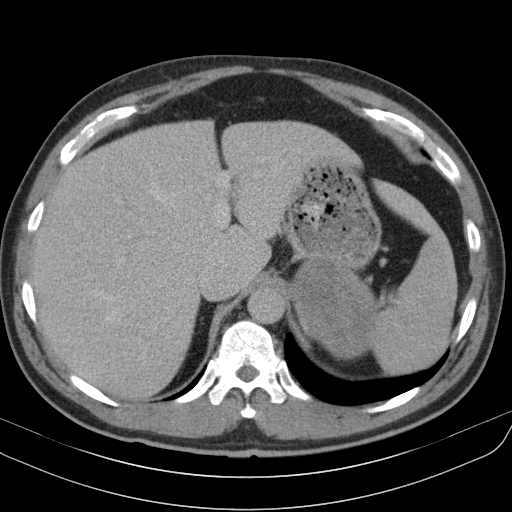
Contrast-enhanced abdominal CT, one axial slice; slice 78 of 91 in the series (ordered by position); reconstruction kernel B31s; 130 kVp; soft-tissue window (W 400 / L 40 HU); 5 mm slice thickness; 512 × 512 image matrix, field of view 370 × 370 mm. Patient: male, 51 years. From the clinical record (not read from this slice): diagnosis: adrenocortical carcinoma; tumour side: left adrenal; tumour size at pathology: 18 cm; Ki-67 index: 40 %; stage (as recorded): 3.
Outlined on this slice (semi-automatic segmentation, software-assisted and operator-edited):
- mass: bounding box [x1, y1, x2, y2] px = [293, 262, 375, 358]